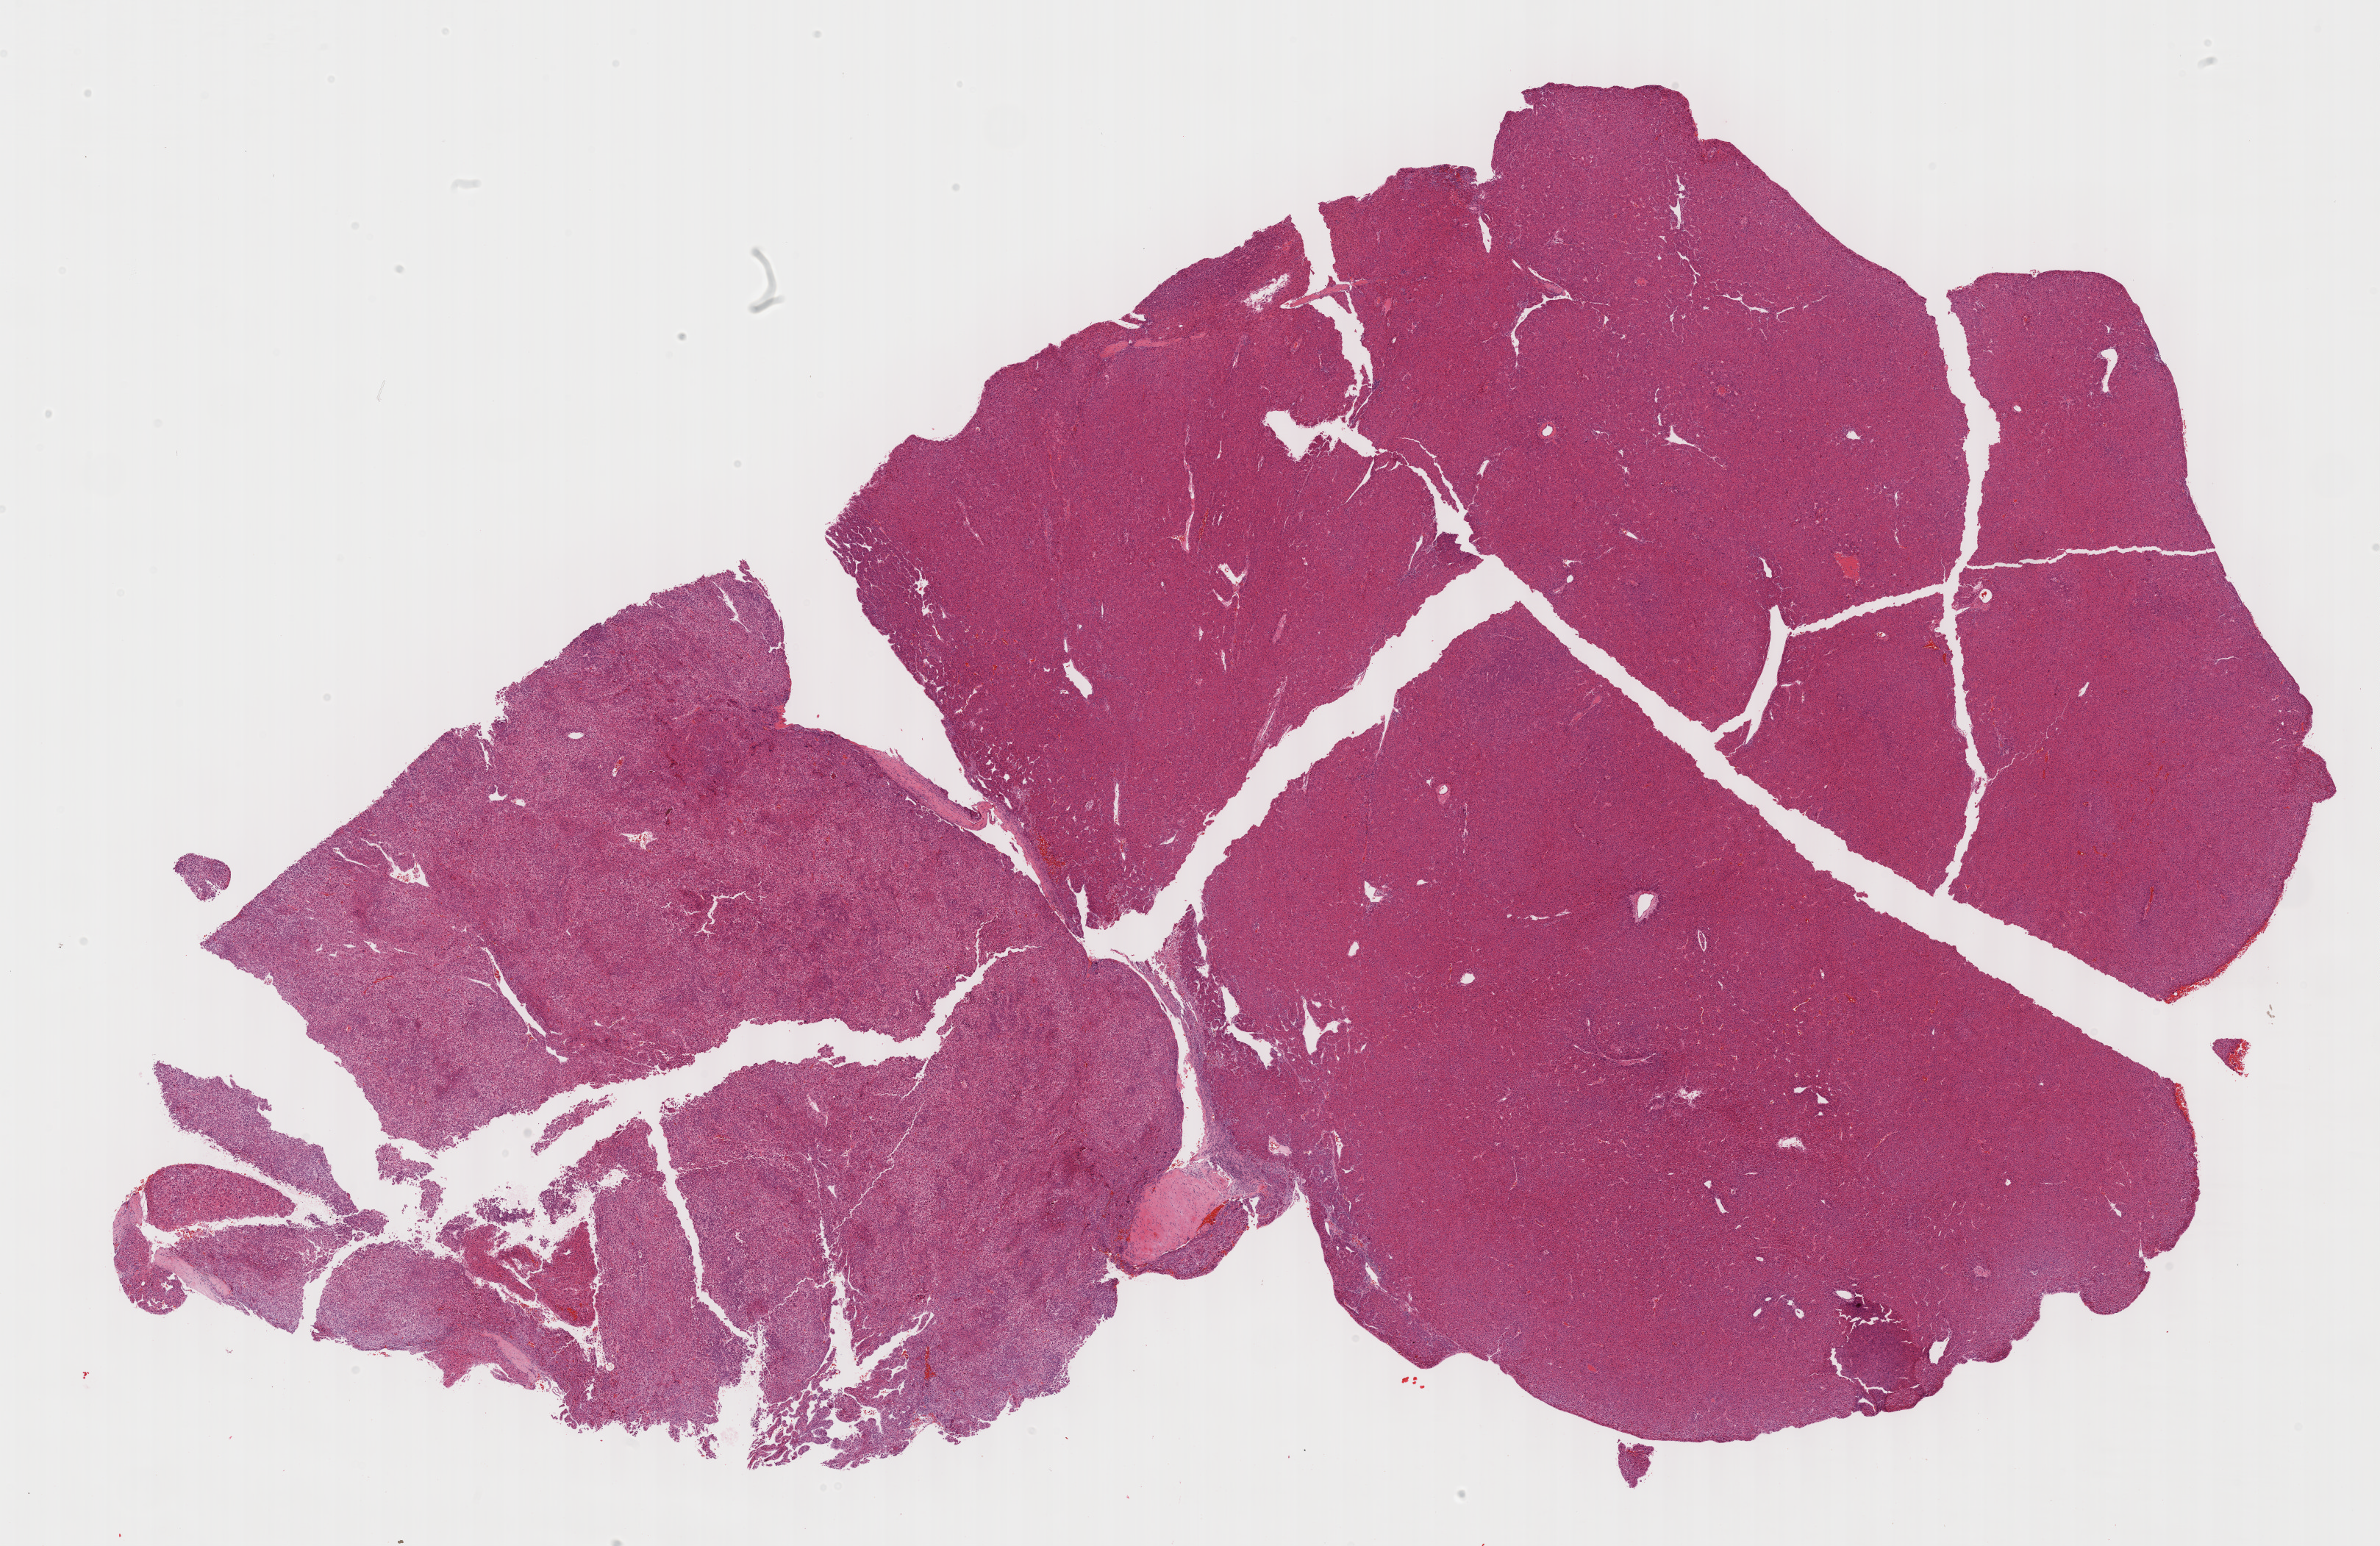
Digitized Hematoxylin and eosin (H&E) stained tissue section (whole slide), shown as a low-resolution overview of the whole scanned area (about 26.2 x 17.0 mm, acquisition: 40x scan); formalin-fixed paraffin-embedded (FFPE) diagnostic section; primary tumour sample from the liver. Male, age 66 years at initial diagnosis. Histologic grade: G3 (poorly differentiated).
• diagnosis: Hepatocellular carcinoma, NOS
• TNM: T2 N0 M0
• AJCC pathologic stage: II